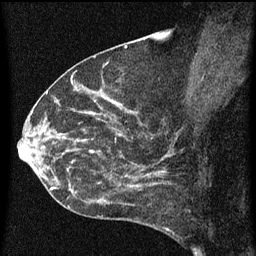
Breast MRI (dynamic contrast-enhanced), one sagittal slice; position 33 of 60 along the scan axis; dynamic contrast-enhanced series, image 2 of 3 at this slice position (ordered by acquisition); 1.5 T; TE 4.2 ms, TR 8 ms; 2 mm slice thickness; 256 × 256 image matrix, field of view 180 × 180 mm. Female patient, age 54 years.
Structures marked on this image (semi-automatic segmentation, software-assisted and operator-edited):
- analysis volume of interest (the breast-tissue region the enhancement analysis was run in; not a lesion): bounding box (x1, y1, x2, y2) in pixels: (49, 138, 164, 209)
- tumour enhancement mask (voxels above the 70 % enhancement threshold inside the analysis volume of interest): (51, 138, 164, 207)